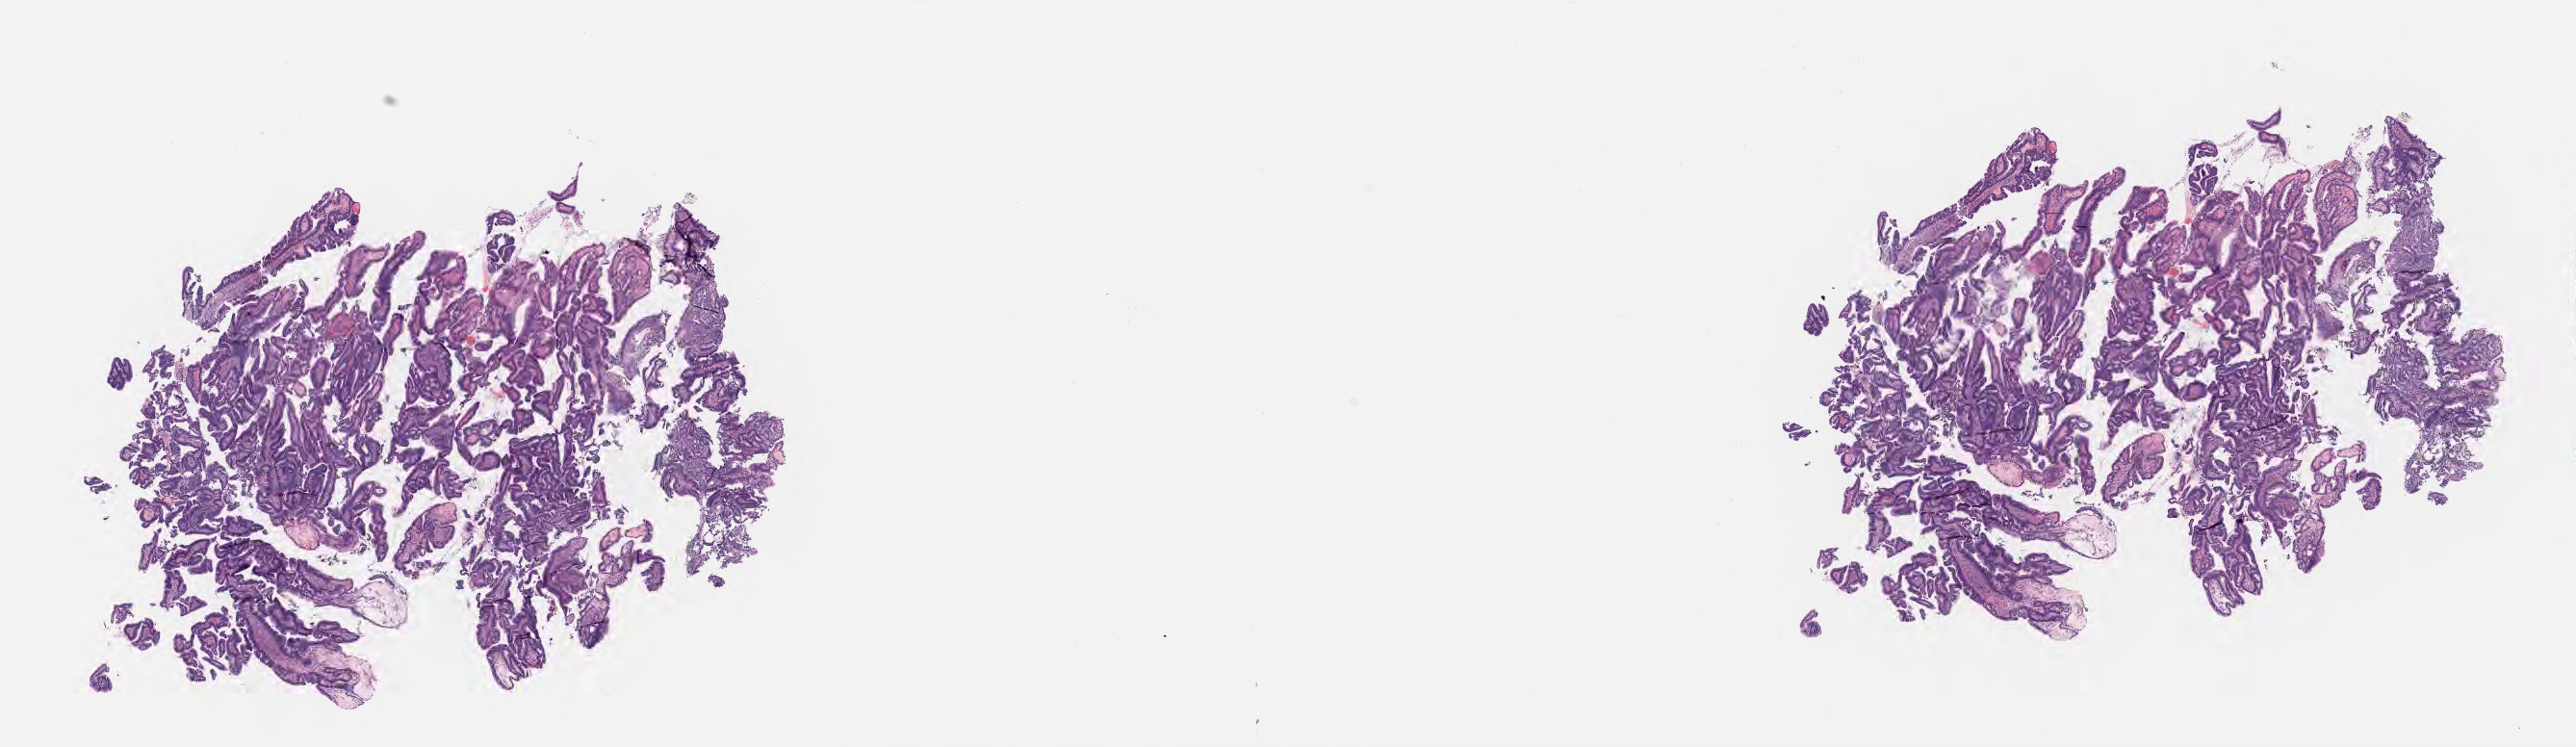
H&E whole-slide image — a low-resolution overview of the entire scanned area, about 21.6 x 6.3 mm. Specimen: tumor tissue. Site: cervix. Patient: female, aged 45.
- diagnosis: Adenocarcinoma, NOS